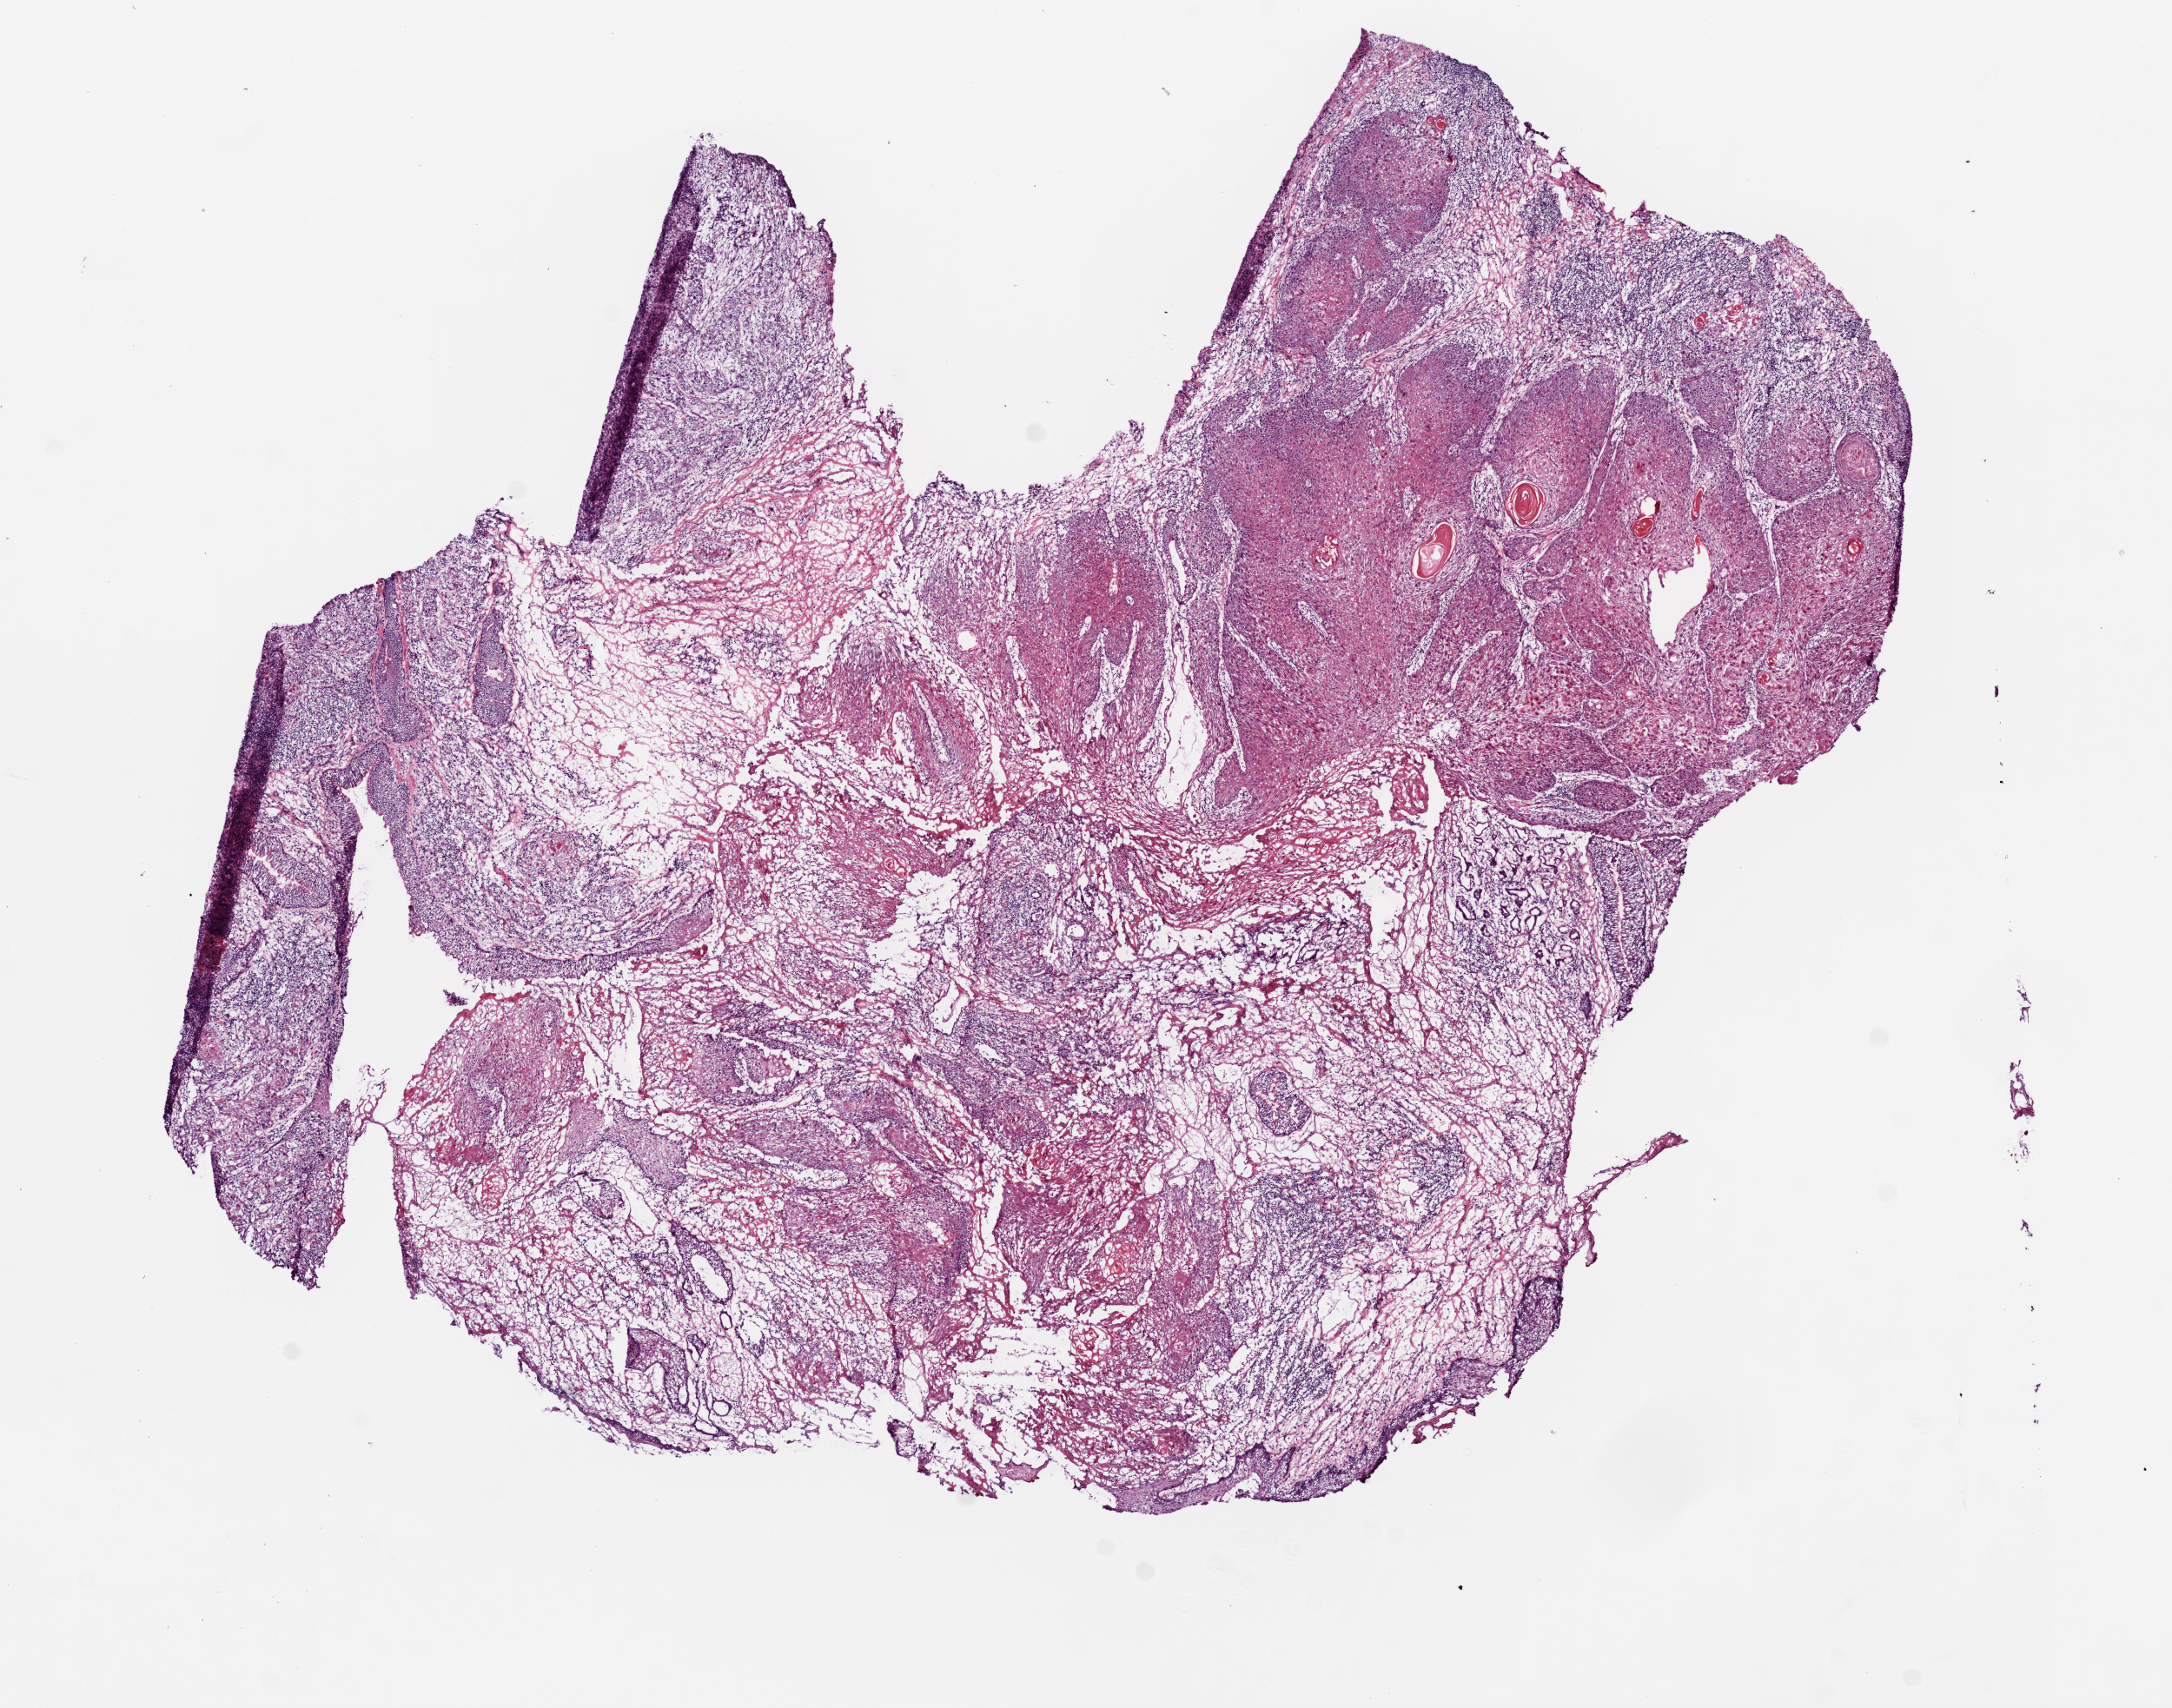
Whole-slide histology image, H&E, shown as a low-resolution overview of the whole scanned area (about 10.0 x 7.9 mm, acquisition: 20x scan). Frozen section. Head and neck, primary tumour sample. Male patient; age at initial diagnosis 53 years. Composition of this section per pathologist review: tumour cells 65%, tumour nuclei 65%.
Pathologic diagnosis: Squamous cell carcinoma, NOS (larynx, NOS).